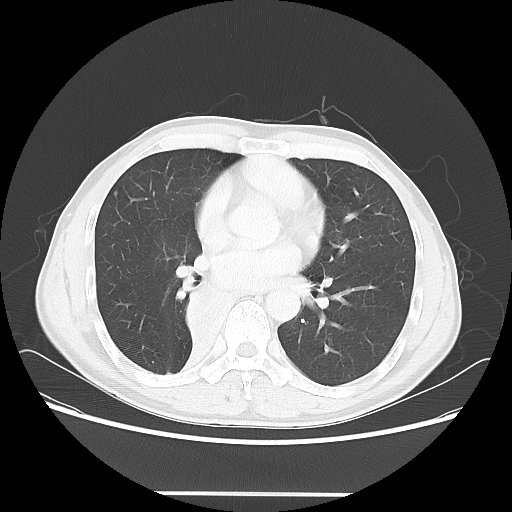
Chest CT, one axial slice. Position 30 of 62 along the scan axis. Lung window (W 1500 / L -600 HU). 5 mm slice thickness. 512 × 512 image matrix, field of view 393 × 393 mm. Patient: male, 47 years. From the clinical record (not read from this slice): clinical TNM (as recorded): T2 N0 M0; histopathological grade: G2.
Structures marked on this image (bounding box drawn by a radiologist):
- lung tumour (recorded histology: squamous cell carcinoma): box from (x=184, y=284) to (x=236, y=347) px